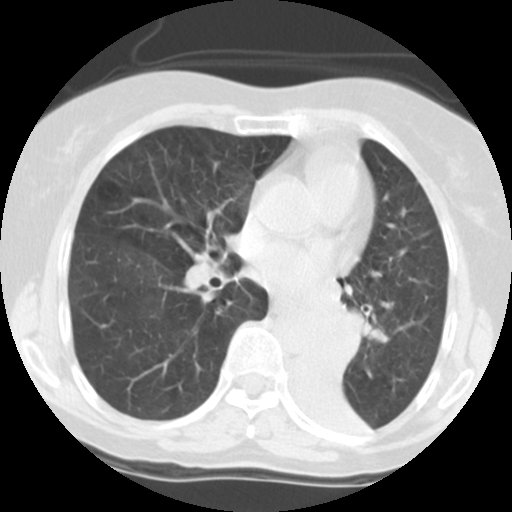
Low-dose screening chest CT, one axial slice; 140 kVp; lung window (W 1500 / L -600 HU); 2.5 mm slice thickness; 512 × 512 image matrix, field of view 280 × 280 mm.
Annotated regions visible in this slice (manually delineated by an expert):
- lesion 1 (tumor, left main bronchus): bounding box (x1, y1, x2, y2) in pixels: (310, 311, 363, 377)